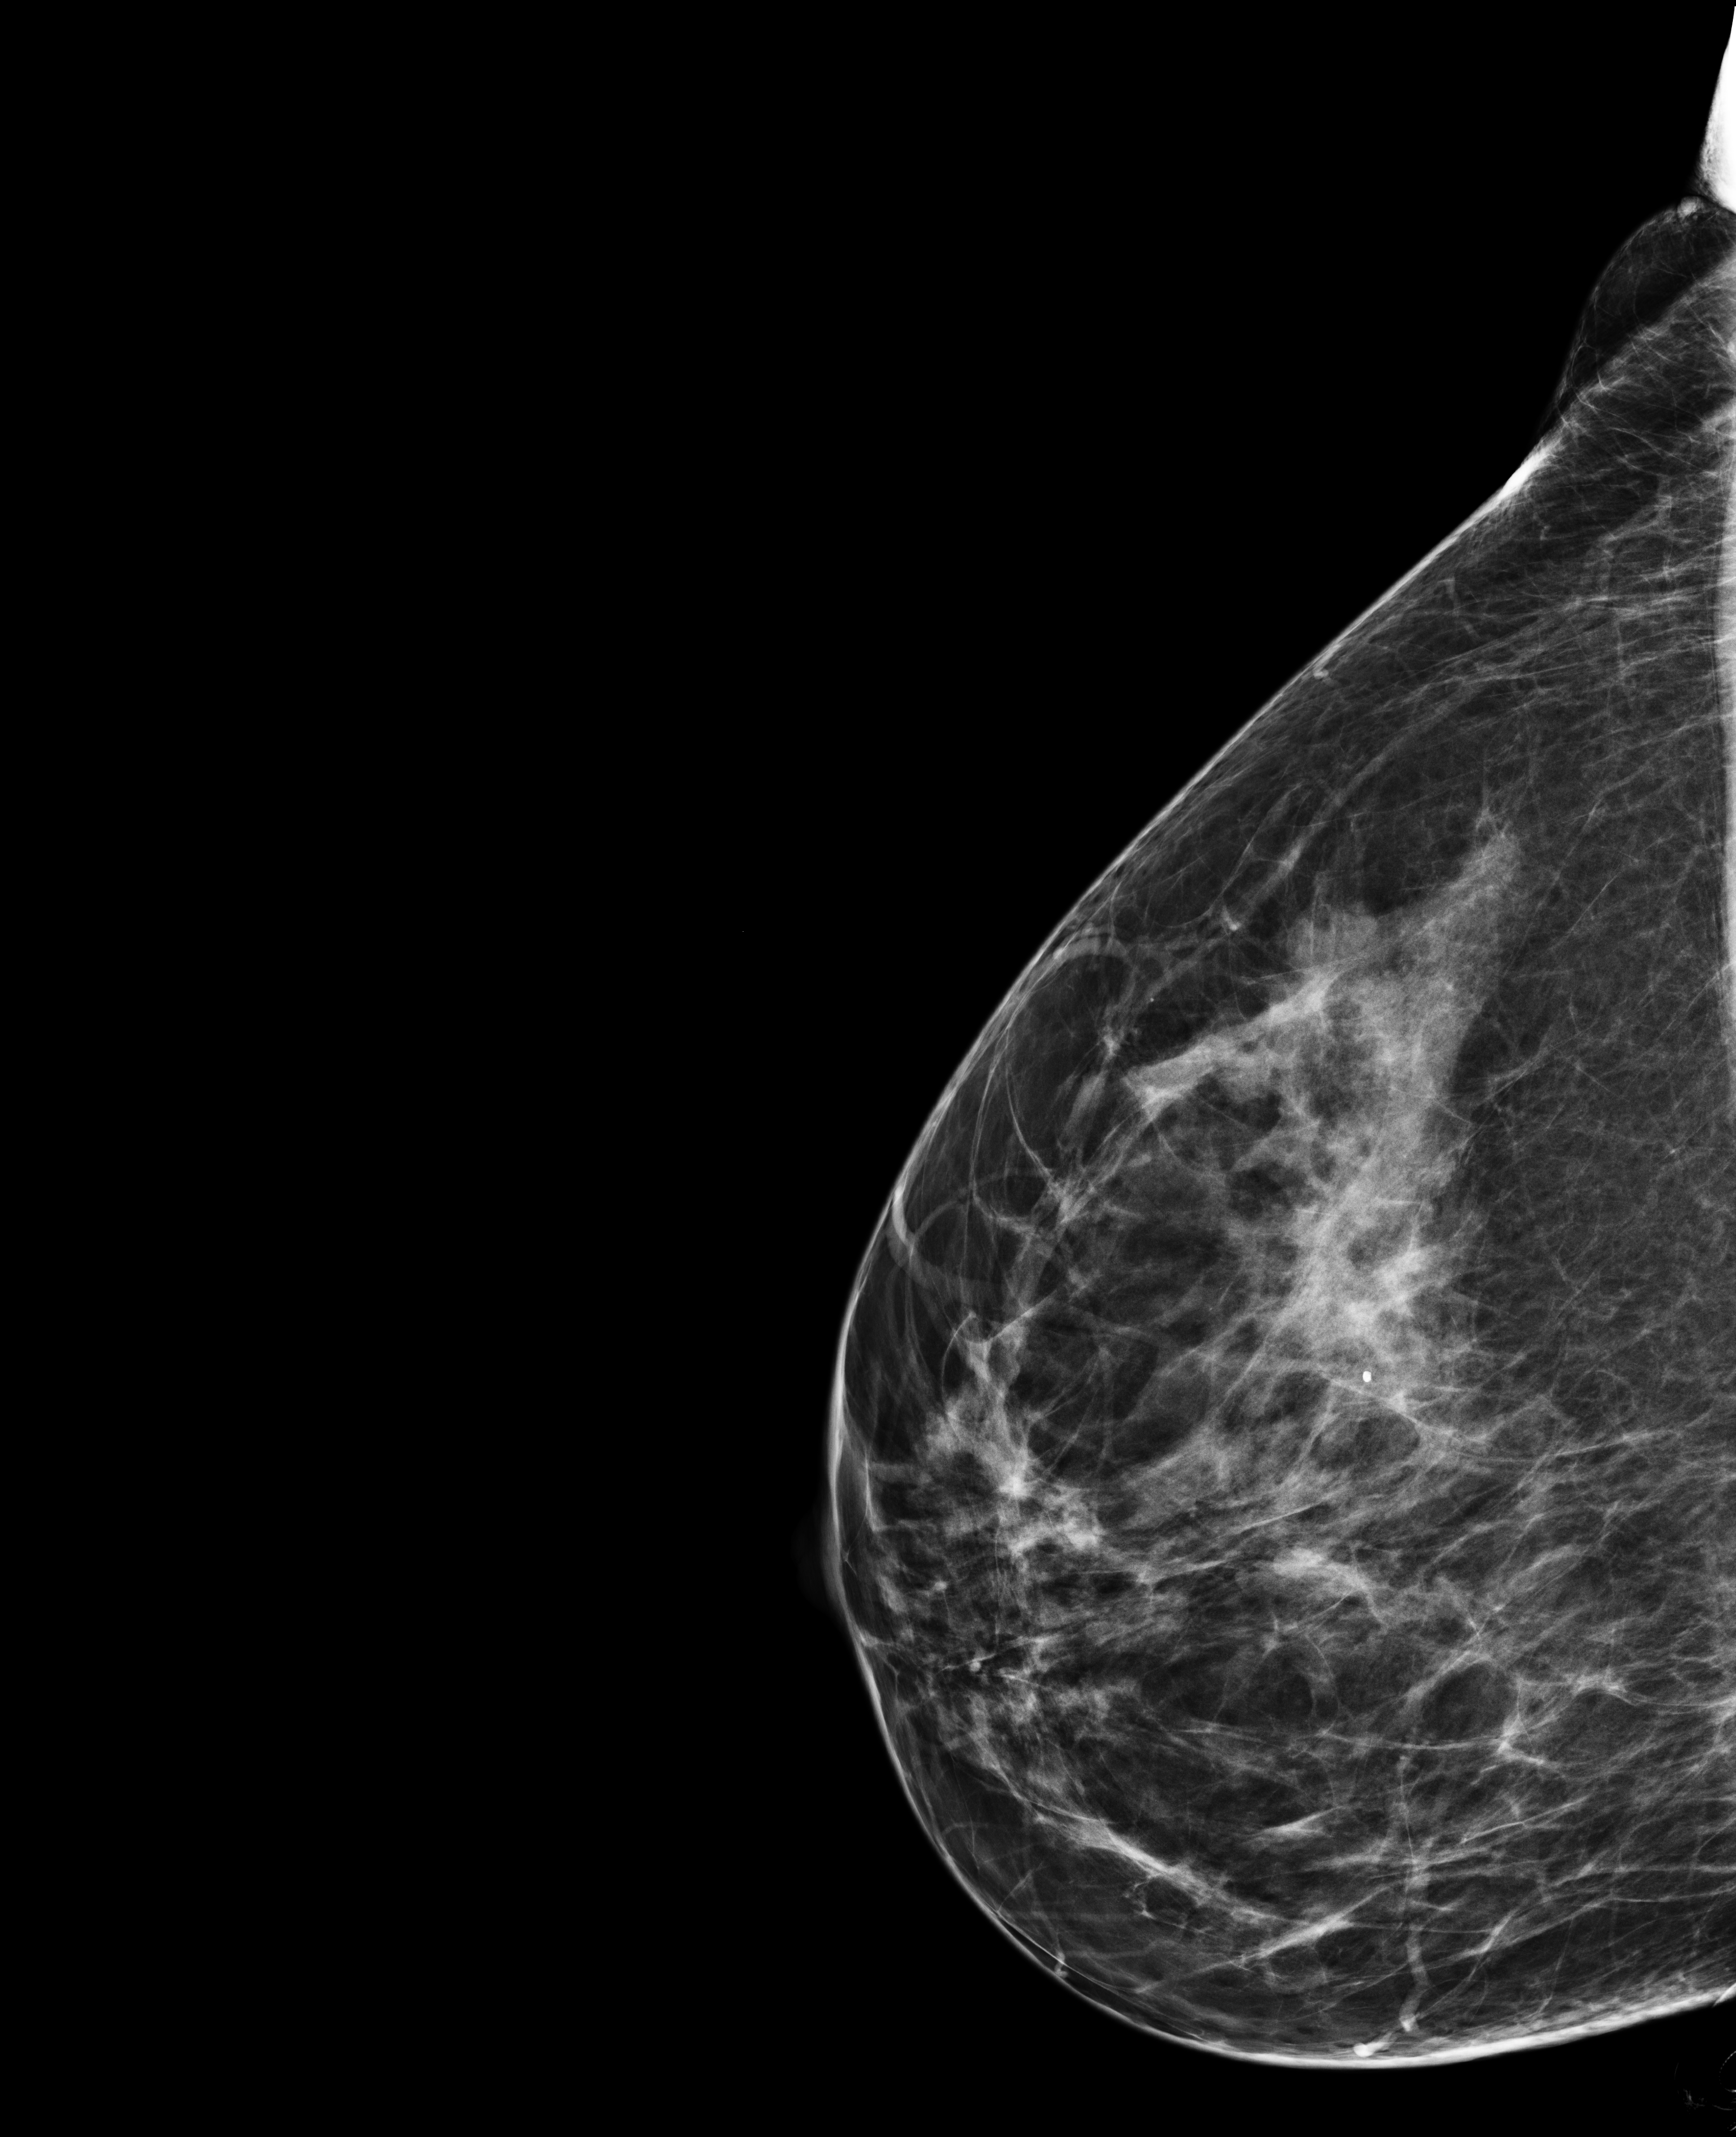
Annual screening mammography examination, system: Selenia Dimensions. Patient: female, 47 years.
Image type: full-field digital mammogram. Breast: right. Projection: laterally exaggerated craniocaudal (XCCL) view. BI-RADS breast density category at the screening exam (both breasts, scale 1–4): 3. Final BI-RADS category for the screening round (tomosynthesis exam, both breasts): category 2. Recall: no recall after this screen.